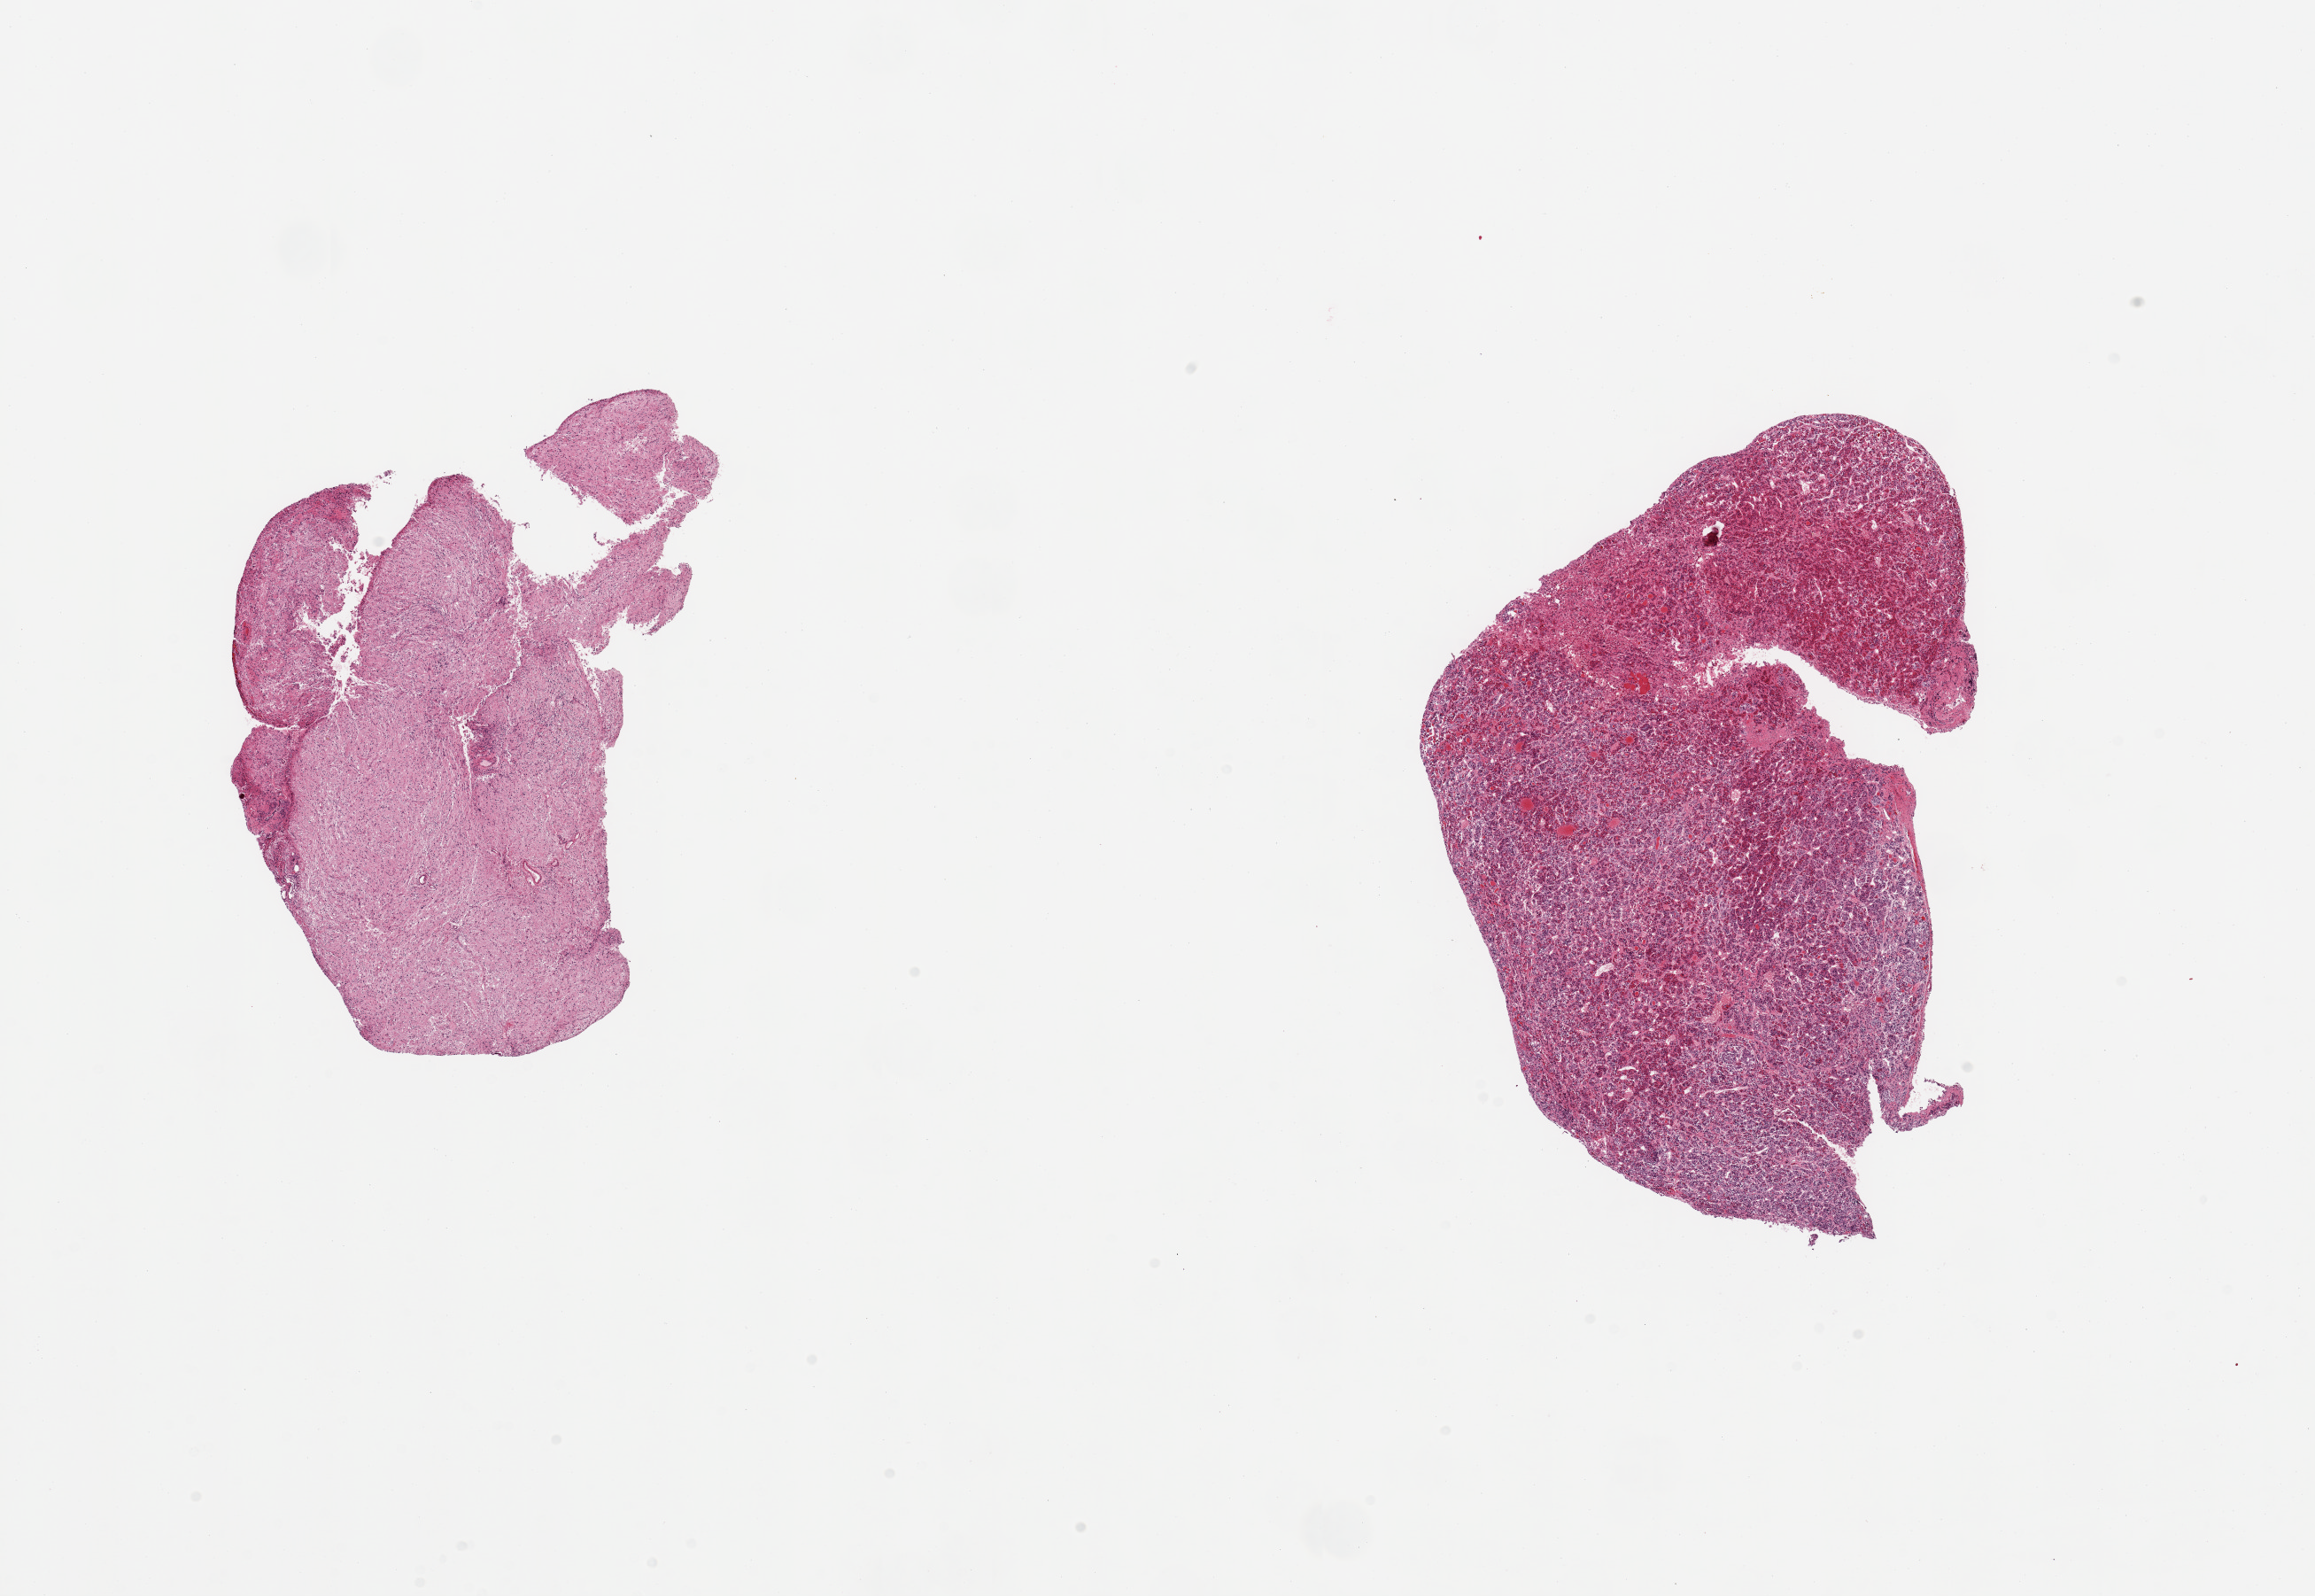
Whole-slide image, hematoxylin and eosin (H&E) stain, low-resolution overview of the scanned area, about 20.7 x 14.3 mm; PAXgene-fixed, paraffin-embedded tissue; section of pituitary (target tissue); donor tissue sample. Donor: male.
* review note (as recorded): 2 pieces: 1 is neurohypophysis, other is adenohypophysis